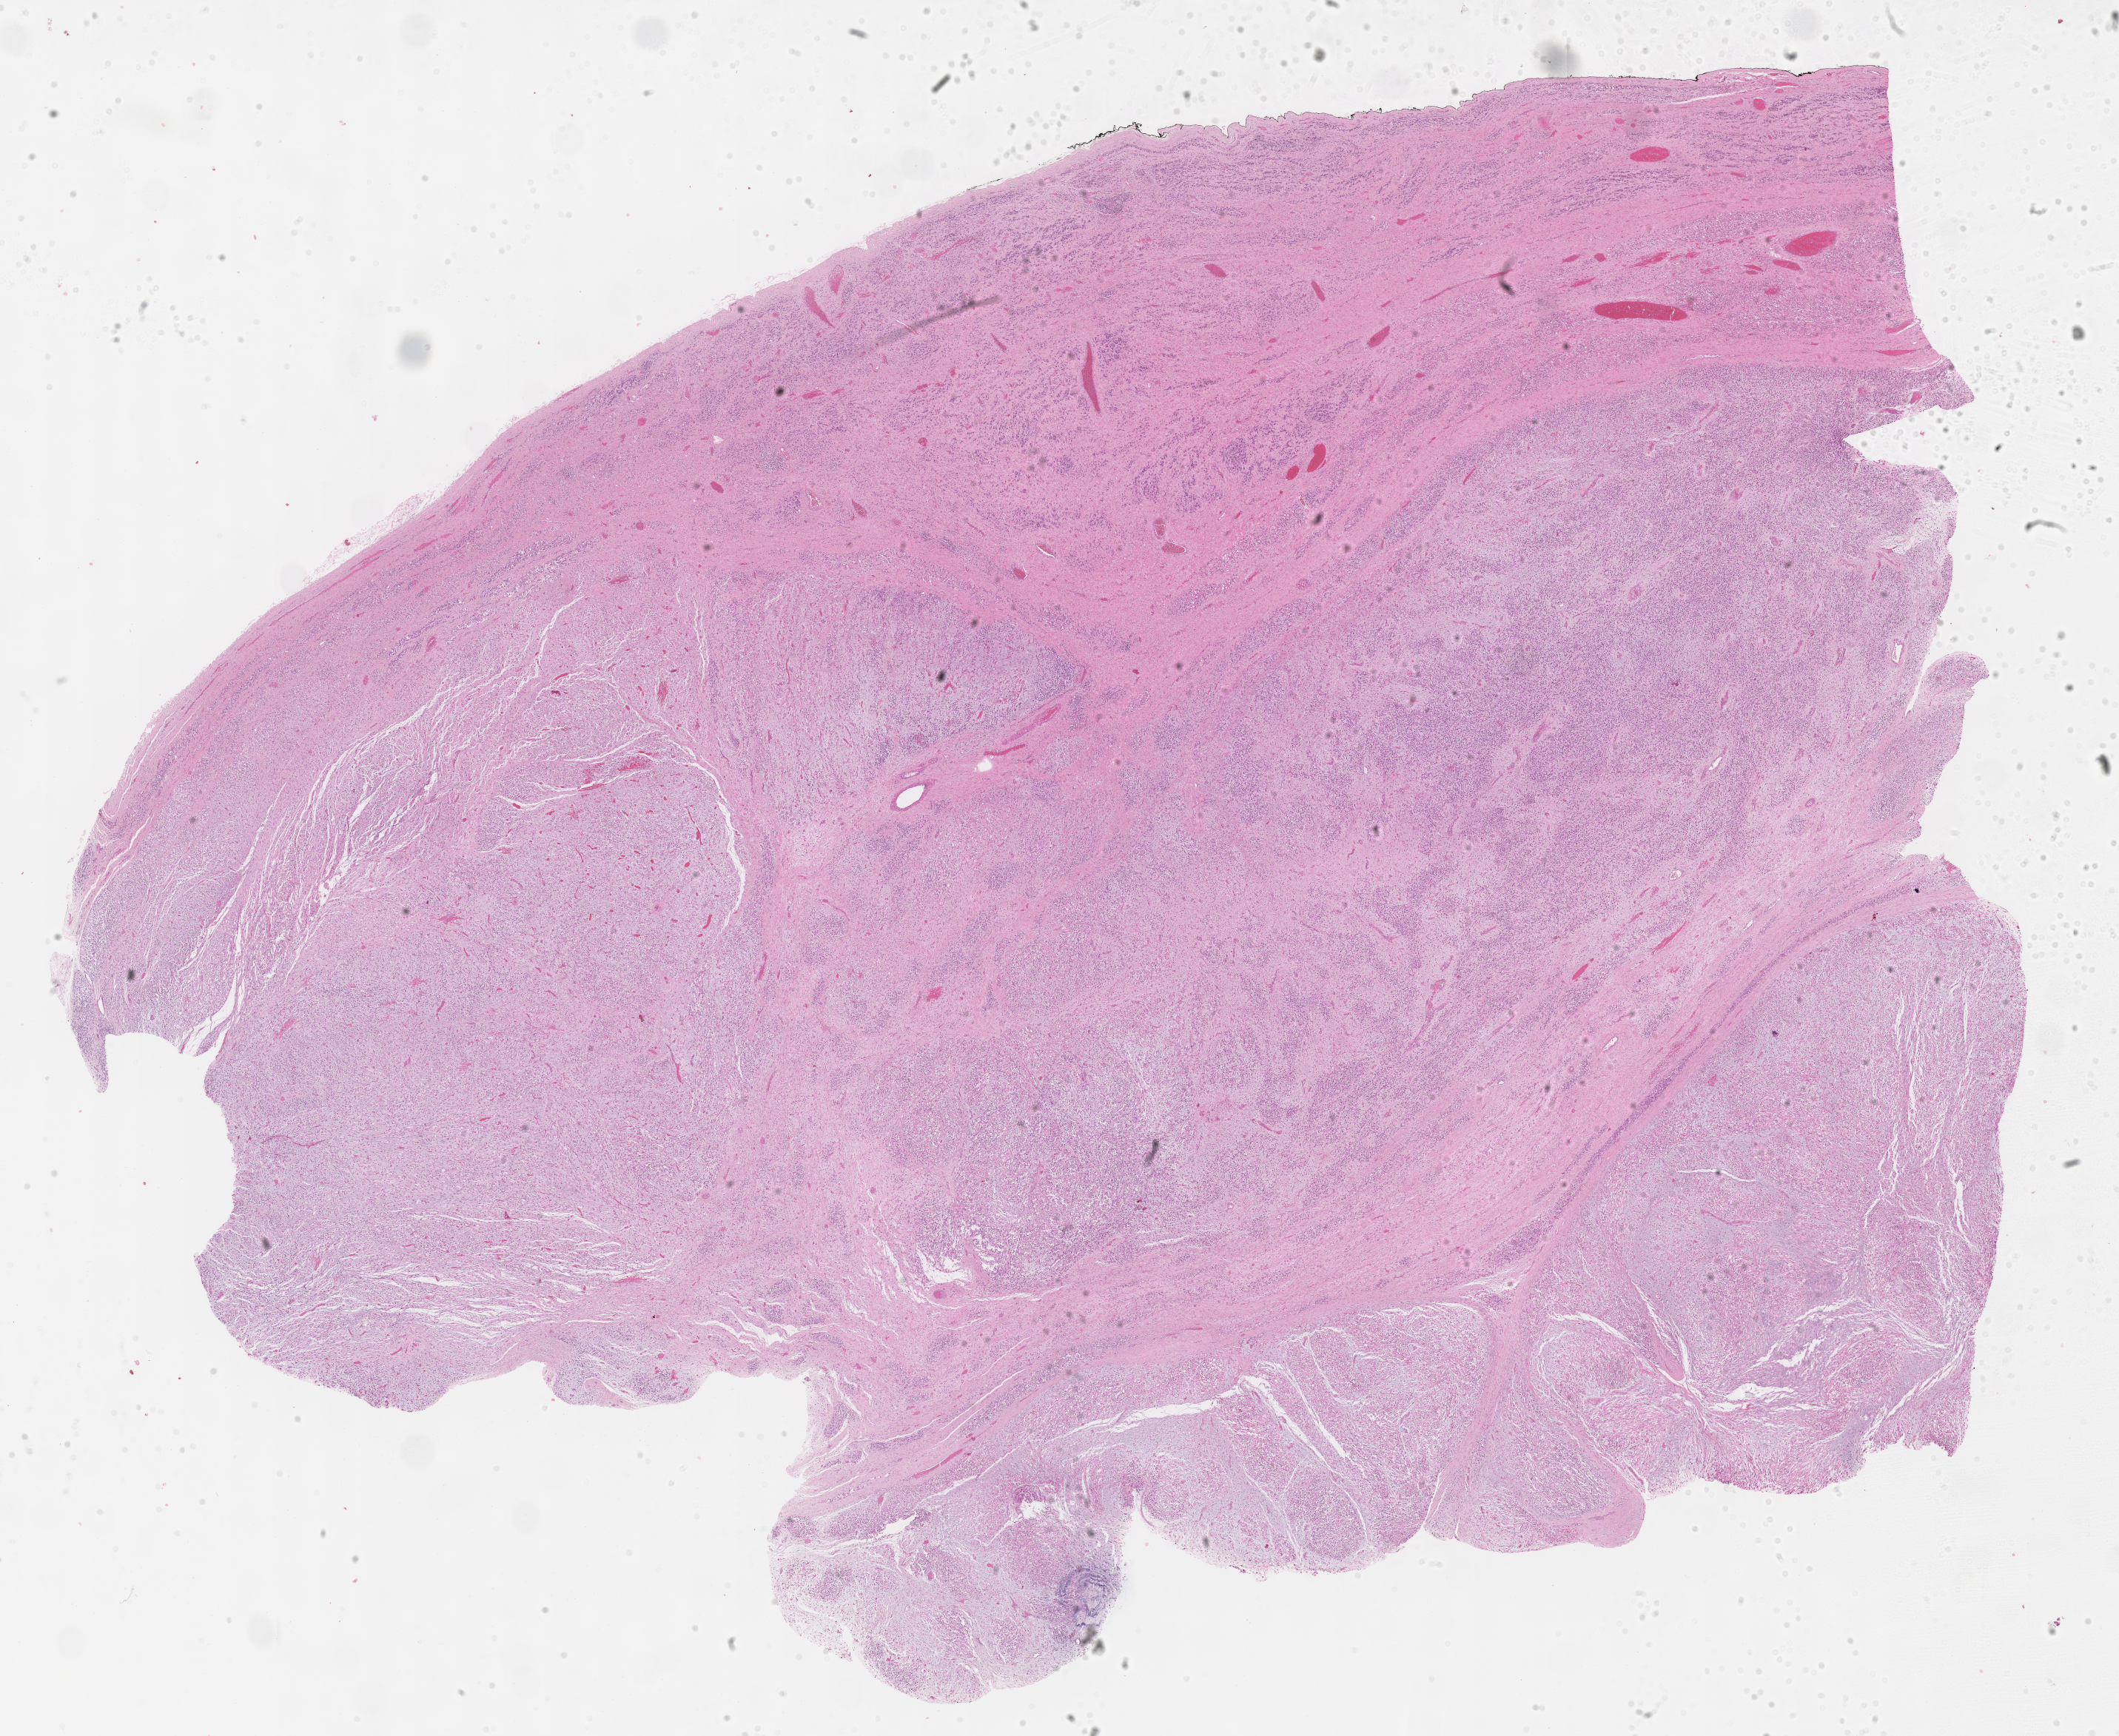
Whole-slide image, haematoxylin and eosin stain of tumor tissue — low-resolution overview of the scanned area, about 23.1 x 19.0 mm; formalin-fixed paraffin-embedded section; sample anatomic site: soft tissue - testicle, right. Male patient, age at diagnosis 7.5 years.
- stage (as recorded): 1
- diagnosis: rhabdomyosarcoma; histological classification: embryonal rhabdomyosarcoma
- metastatic status at presentation (as recorded): non-metastatic (unconfirmed)